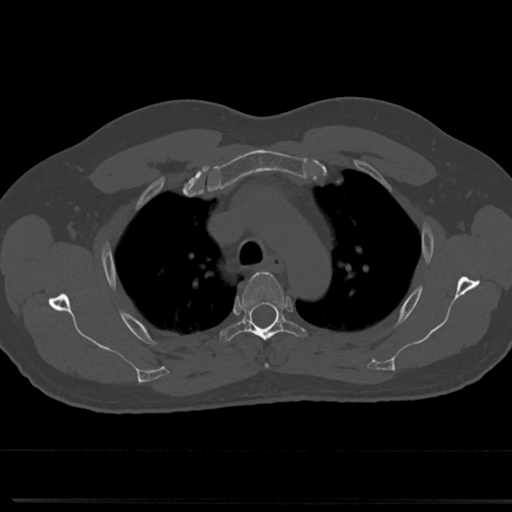
CT including the spine, one axial slice; position 554 of 817 along the scan axis; 120 kVp; bone window (W 1800 / L 400 HU); 512 × 512 image matrix, field of view 355 × 355 mm. Patient: male, 61 years. From the clinical record (not read from this slice): primary cancer: prostate.
Annotated regions visible in this slice (semi-automatic segmentation, software-assisted and operator-edited):
- T3 vertebra: box from (x=264, y=363) to (x=269, y=368) px
- T4 vertebra: (x=219, y=272)–(x=306, y=343)